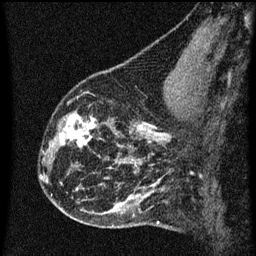
Breast MRI (dynamic contrast-enhanced), one sagittal slice; slice 21 of 60 in the series (ordered by position); dynamic contrast-enhanced series, image 2 of 3 at this slice position (ordered by acquisition); 1.5 T; TE 4.2 ms, TR 8 ms; 2 mm slice thickness; 256 × 256 image matrix, field of view 180 × 180 mm. Female patient, age 43 years.
Structures marked on this image (semi-automatic segmentation, software-assisted and operator-edited):
- analysis volume of interest (the breast-tissue region the enhancement analysis was run in; not a lesion): bounding box (x1, y1, x2, y2) in pixels: (55, 104, 104, 153)
- tumour enhancement mask (voxels above the 70 % enhancement threshold inside the analysis volume of interest): (59, 114, 100, 147)